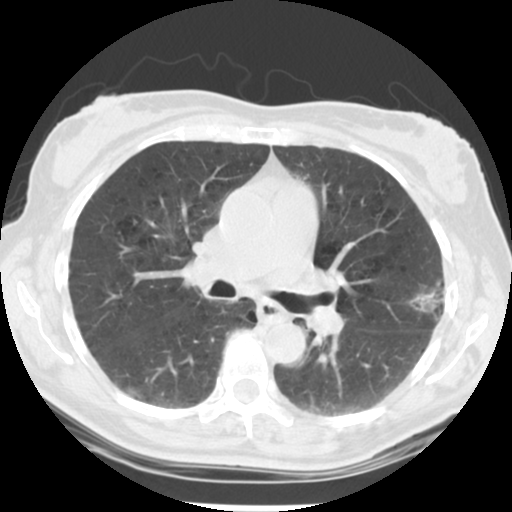
Low-dose screening chest CT, one axial slice. Slice 129 of 223 in the series (ordered by position). Reconstruction kernel STANDARD. 120 kVp. Lung window (W 1500 / L -600 HU). 512 × 512 image matrix, field of view 302 × 302 mm.
Structures marked on this image (manually delineated by an expert):
- lesion 1 (tumor, upper lobe of left lung): bounding box [x1, y1, x2, y2] px = [409, 281, 445, 321]